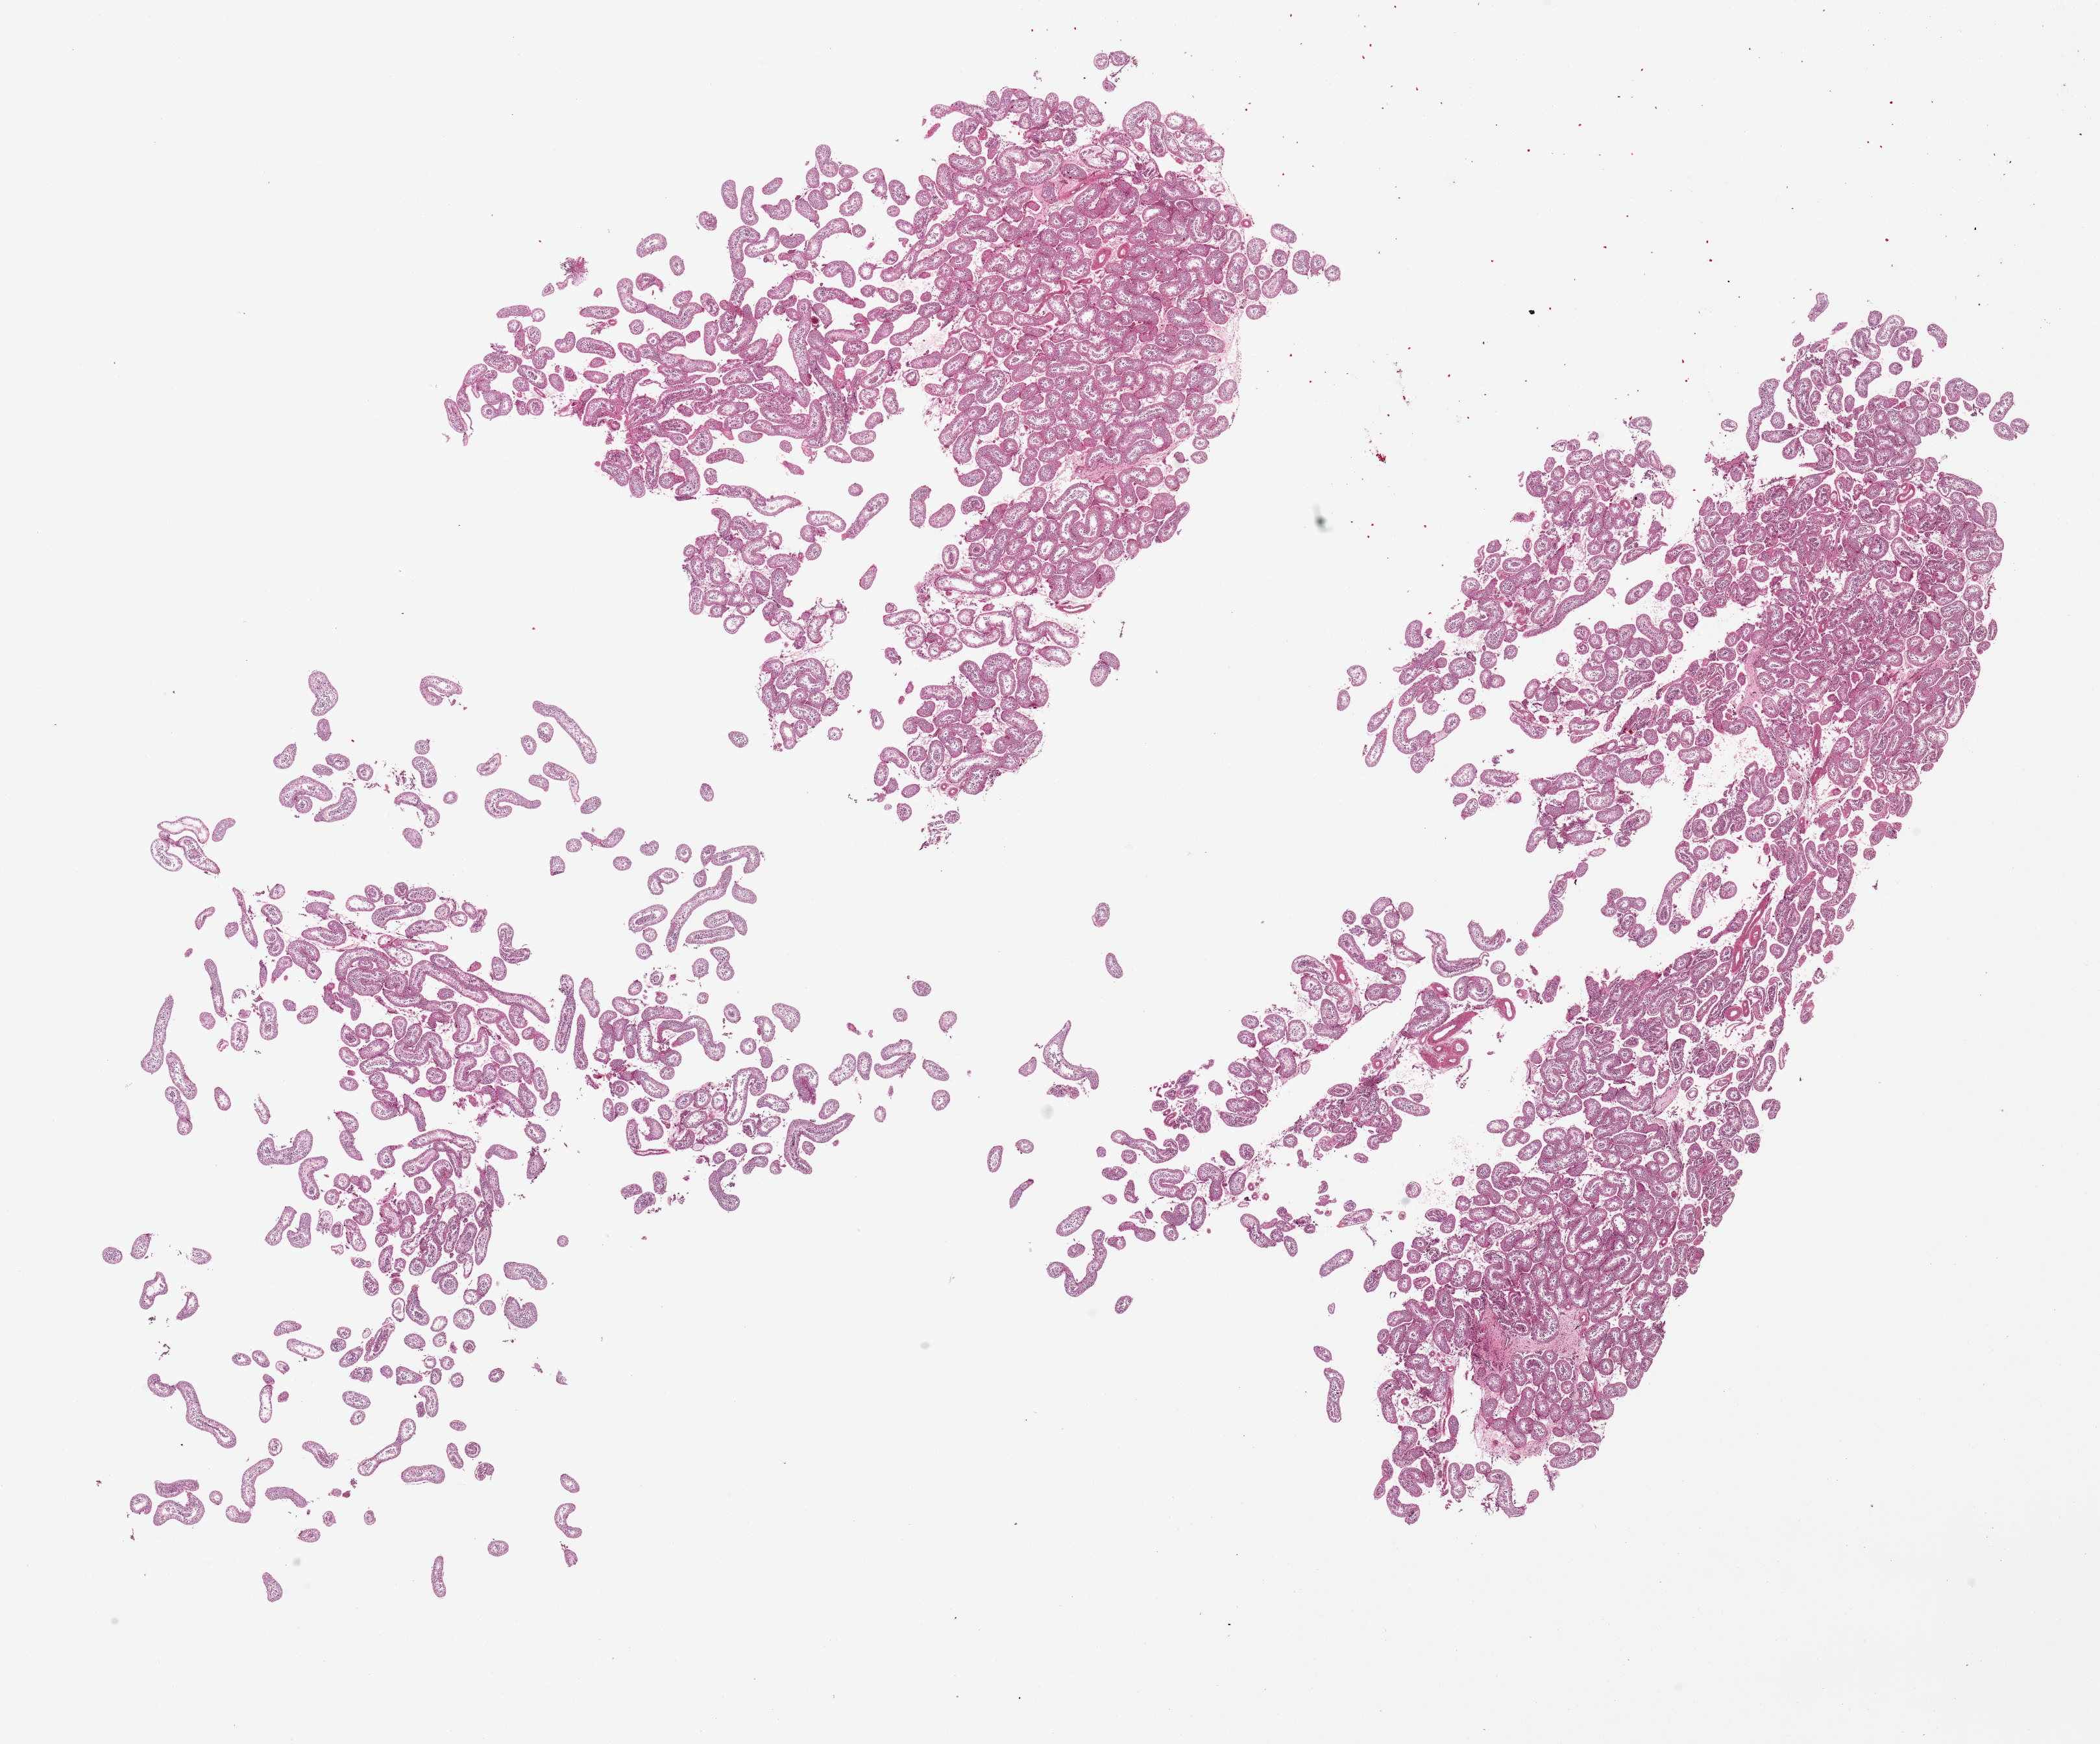
Hematoxylin and eosin (H&E) whole-slide image, brightfield — a low-resolution overview of the entire scanned area, about 25.6 x 21.3 mm (acquisition: 20x scan), PAXgene-fixed, paraffin-embedded tissue, target tissue: testis, tissue donor sample. Donor: male.
• reviewer comment on this tissue sample: 2 pieces, fragmented; reduced spermatogenesis